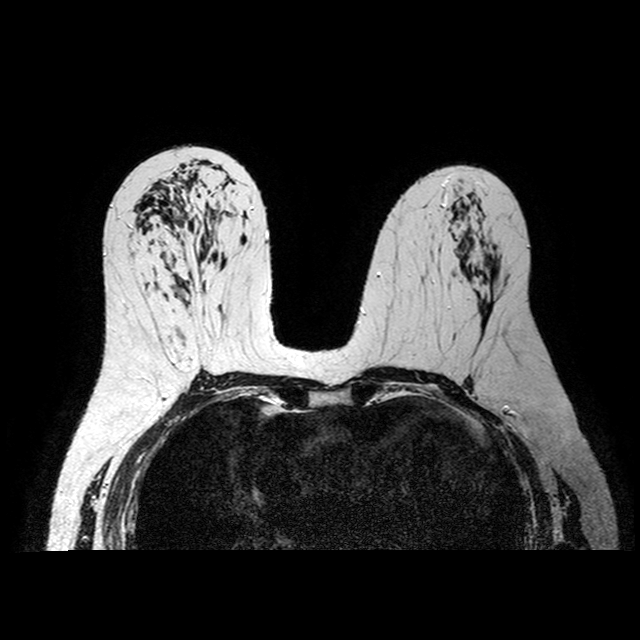
MRI of the breasts; 2 images, each one mid-volume slice chosen by position.
Image 1: axial T2-weighted / STIR image, slice 43 of 84, 2 mm slice thickness.
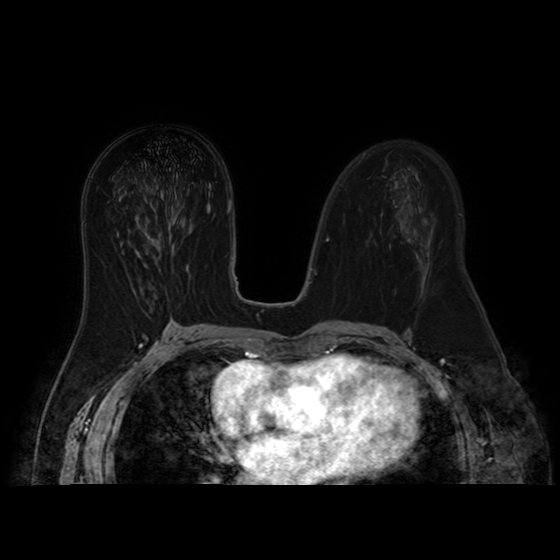
Image 2: post-contrast dynamic axial slice, series "AX BLISS_AUTO SENSE", slice 43 of 84, dynamic phase 5 of 8, 4 mm slice thickness.
Pathology recorded for this patient (not read from these images): pathology diagnosis: benign fibrosis (left breast).